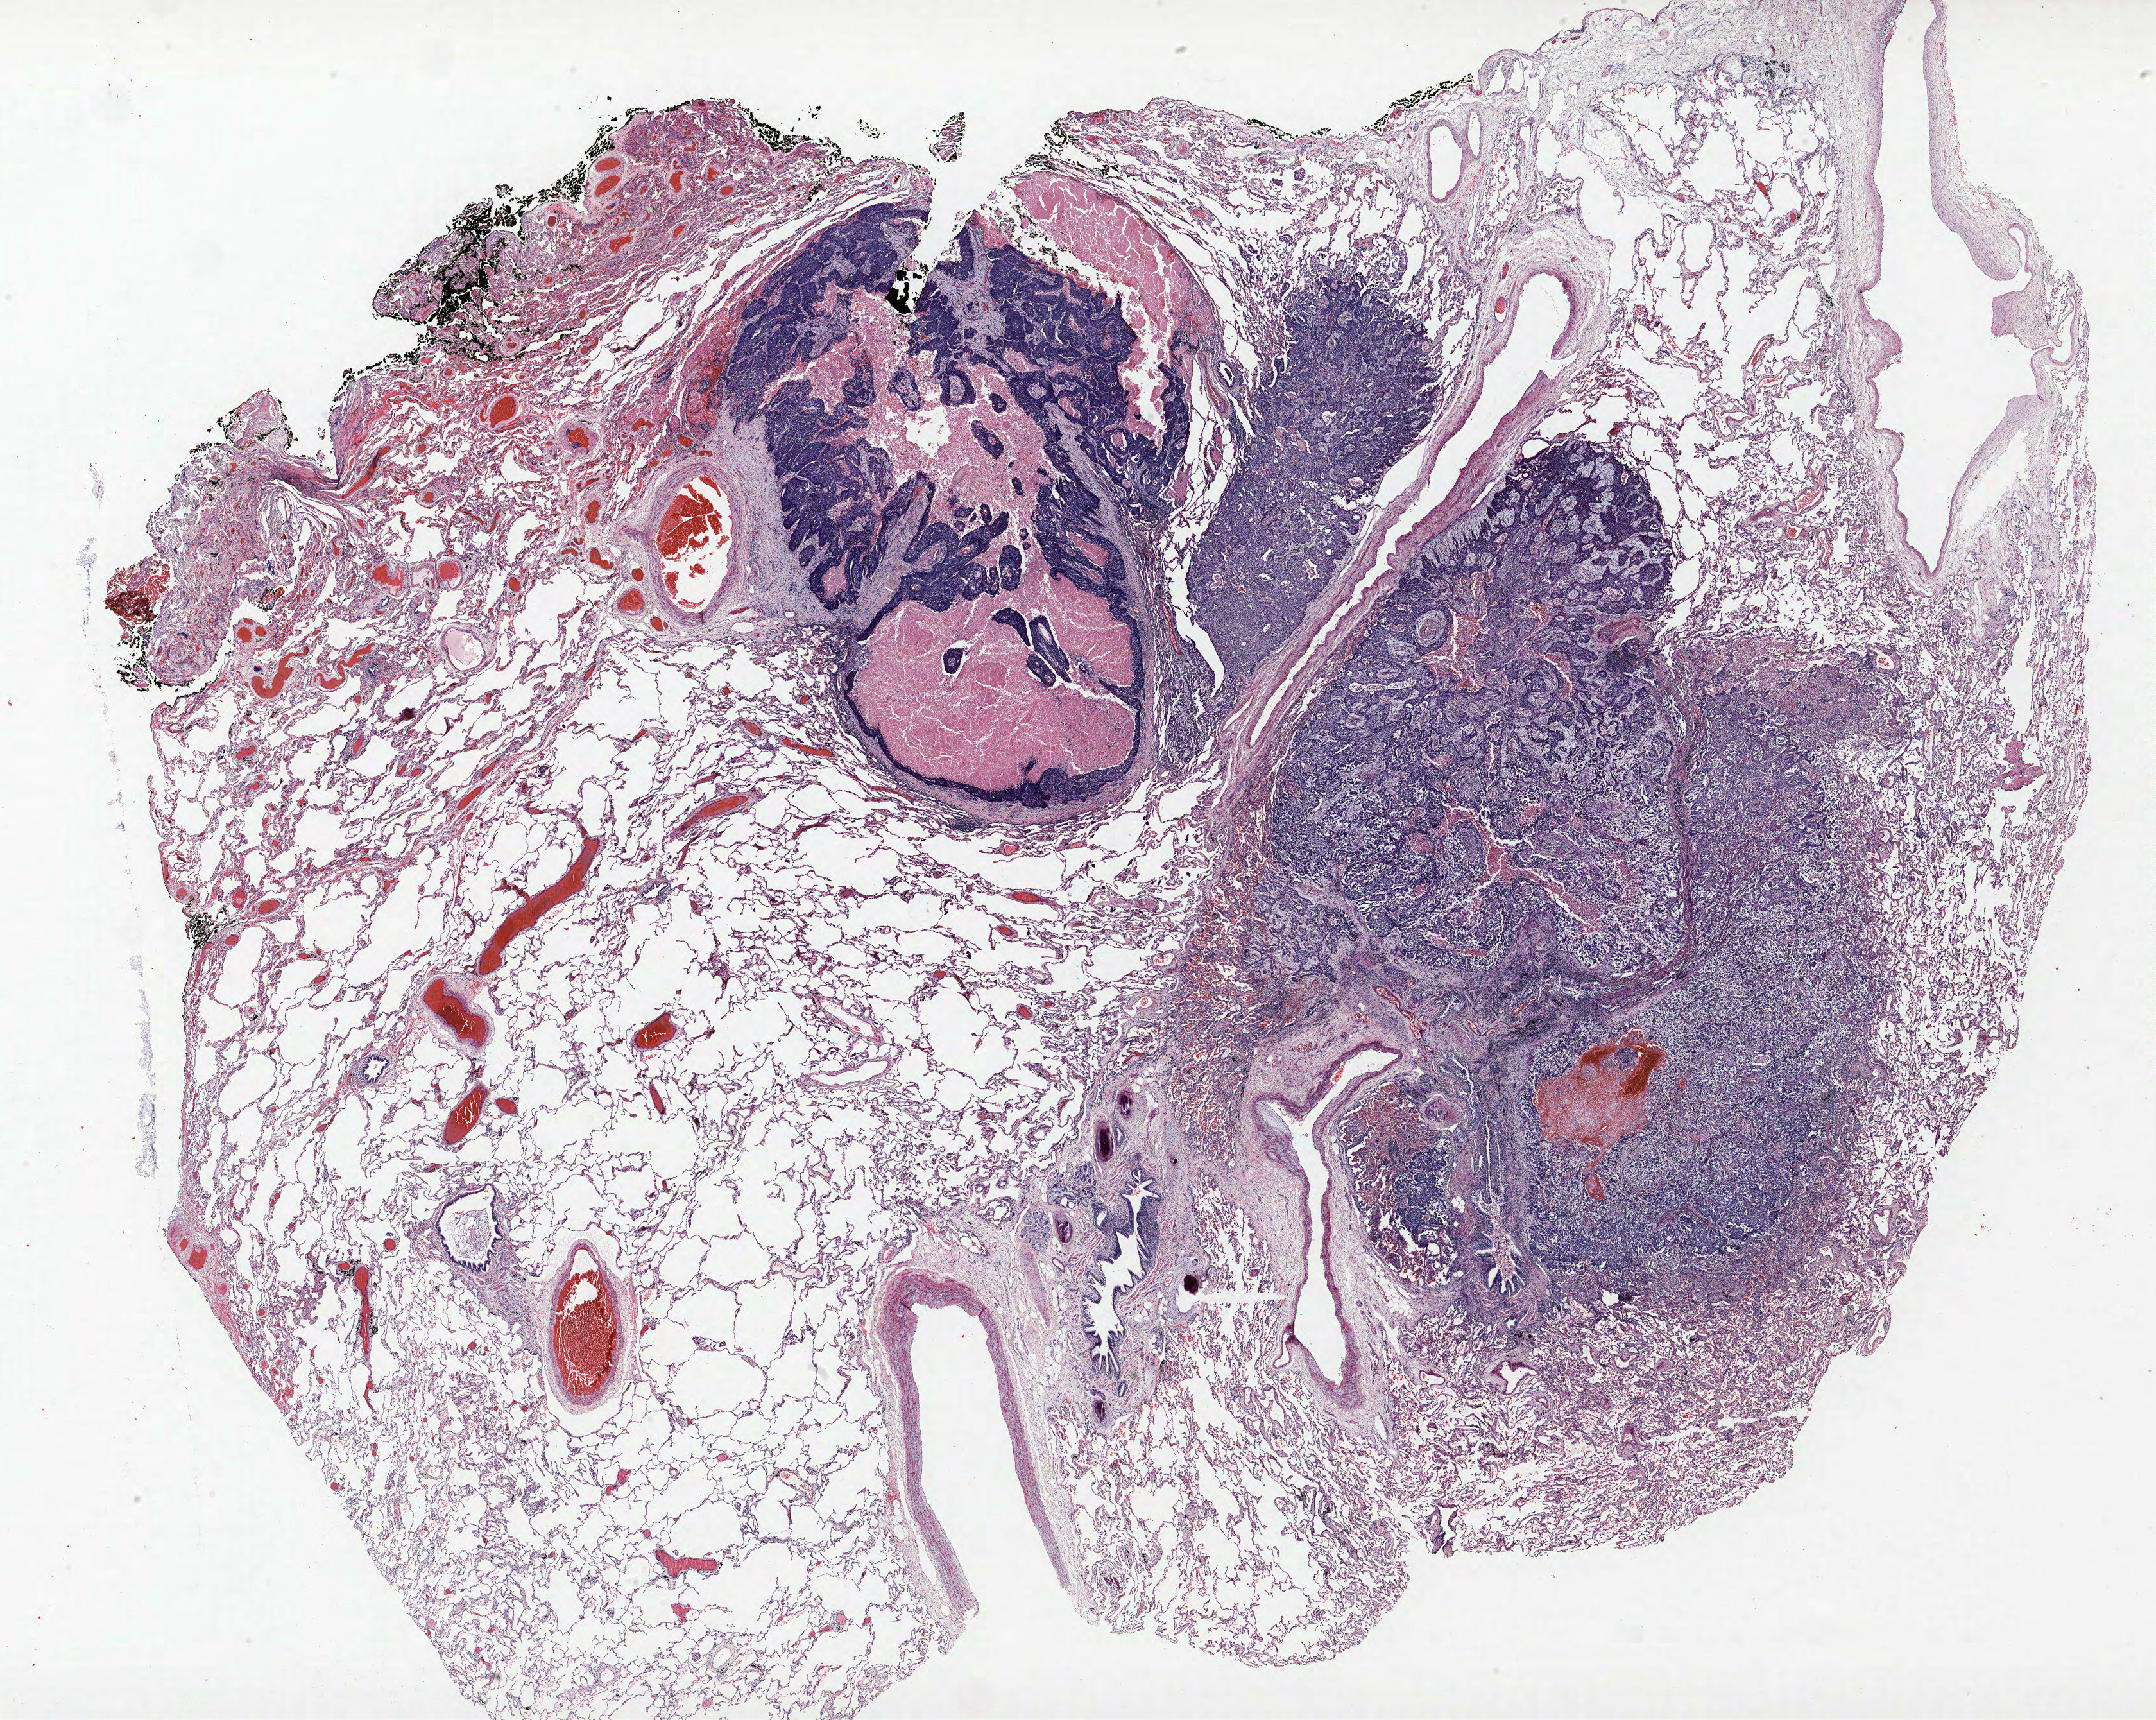
Hematoxylin and eosin (H&E) stained whole-slide image — low-resolution overview of the scanned area, about 26.9 x 21.4 mm. FFPE section. Lung. Female, age 62 at enrolment. Former smoker at enrolment. Grade: moderately differentiated (G2).
Stage (AJCC 6th edition): IA. Tumour size (pathology): 22 mm. Participant's lung-cancer diagnosis: Large cell carcinoma, NOS. Primary tumour location (clinical record): right lower lobe. ICD-O-3 topography: lower lobe of lung (C34.3).